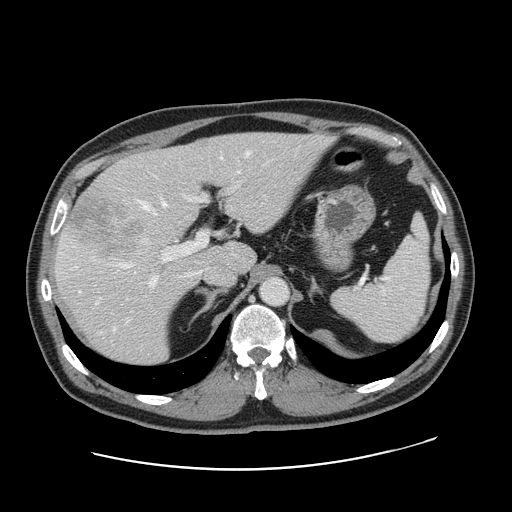
Contrast-enhanced abdominal CT, one axial slice. Slice 111 of 178 in the series (ordered by position). Intravenous contrast given. Soft-tissue window (W 400 / L 40 HU). 2.5 mm slice thickness. 512 × 512 image matrix. Male patient, age 63 years. Case-level facts recorded for this patient, not image findings: diagnosis: colorectal cancer liver metastases, imaged before liver resection; multiple liver metastases: yes; largest metastasis: 8 cm.
Outlined on this slice (outlined manually by an expert reader):
- hepatic veins: box from (x=124, y=152) to (x=249, y=266) px
- liver: (x=56, y=133)–(x=328, y=367)
- planned liver remnant (the part of the liver to remain after resection): (x=132, y=133)–(x=327, y=273)
- portal vein (with intrahepatic branches): (x=145, y=192)–(x=222, y=286)
- liver metastasis: (x=68, y=198)–(x=142, y=259)